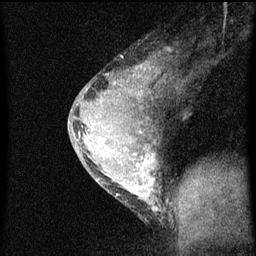
Breast MRI (dynamic contrast-enhanced), one sagittal slice; dynamic contrast-enhanced series, image 2 of 3 at this slice position (ordered by acquisition); 1.5 T; TE 4.2 ms, TR 8 ms; 2 mm slice thickness; 256 × 256 image matrix, field of view 180 × 180 mm. Female patient, age 33 years.
Outlined on this slice (semi-automatic segmentation, software-assisted and operator-edited):
- analysis volume of interest (the breast-tissue region the enhancement analysis was run in; not a lesion): box from (x=69, y=62) to (x=174, y=211) px
- tumour enhancement mask (voxels above the 70 % enhancement threshold inside the analysis volume of interest): (x=80, y=66)–(x=158, y=211)